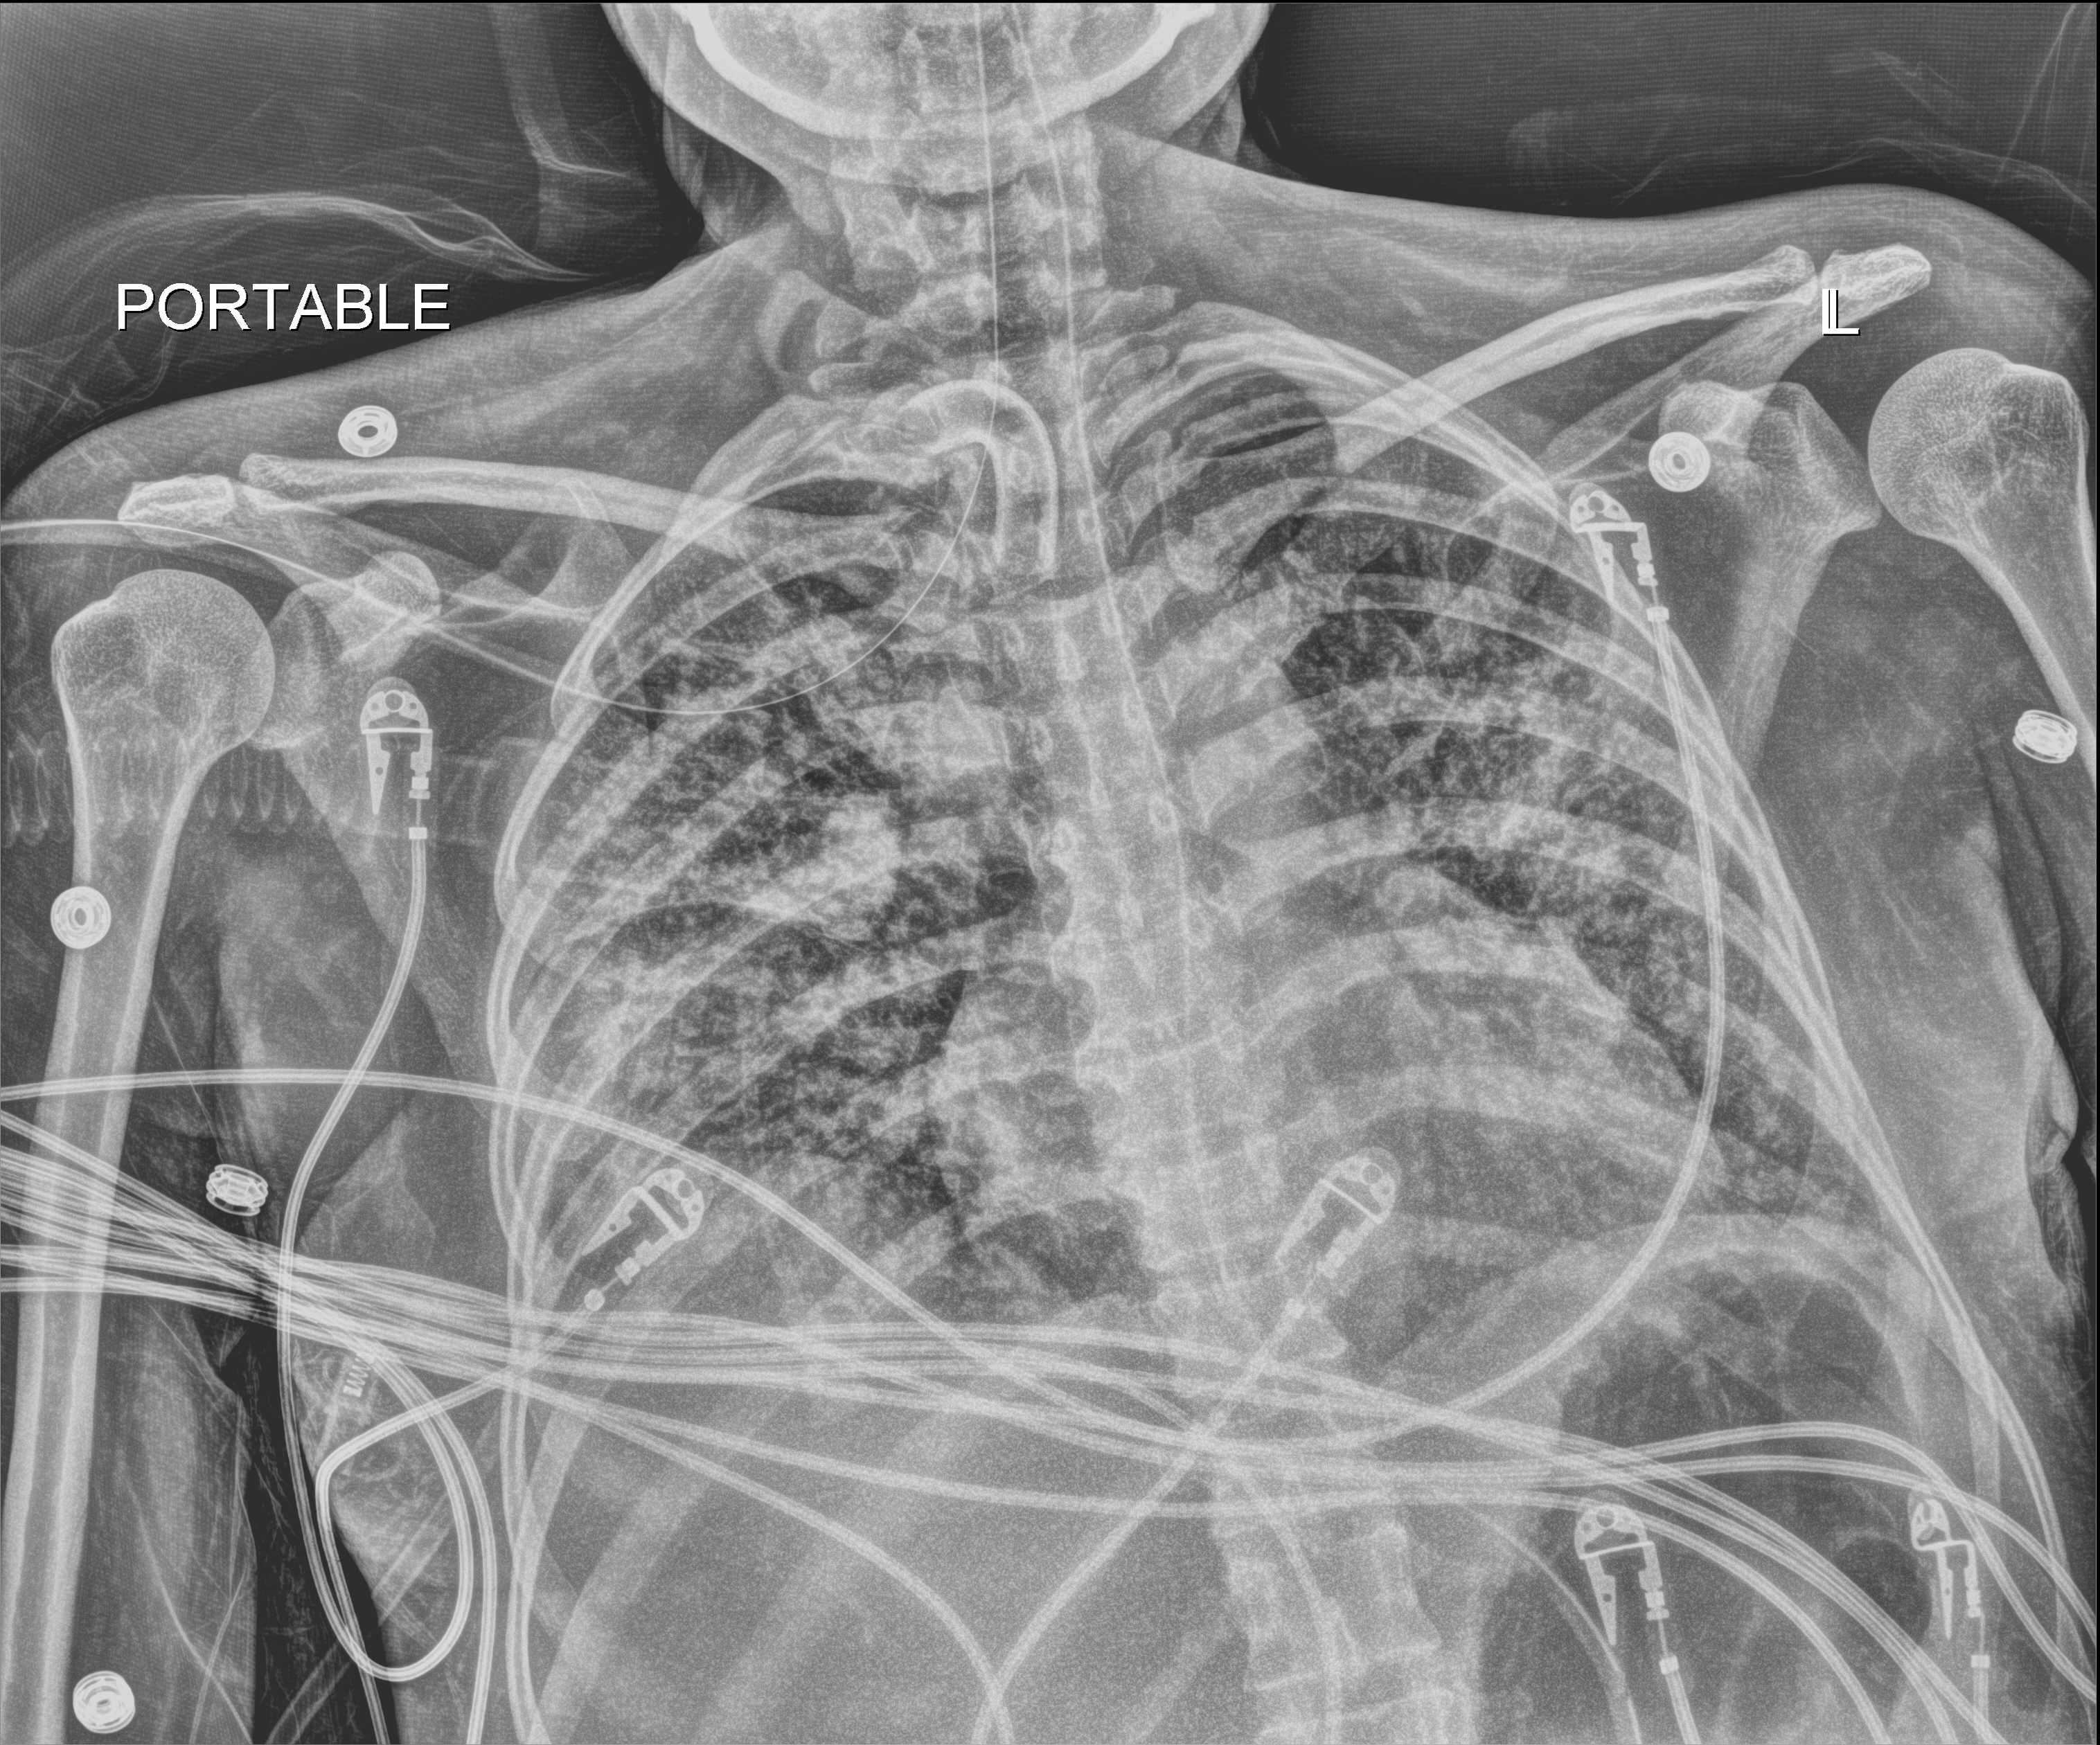
Chest X-ray (portable), anteroposterior (AP) projection. Female patient hospitalised with COVID-19, age 18–59 years.
From the hospital-stay record, not from the radiograph (when in the stay this image was taken is not recorded): mechanically ventilated during this hospital stay: yes; other chronic lung disease (admission record): no.